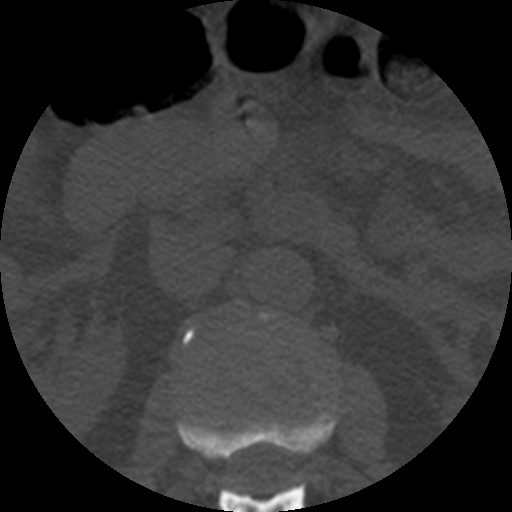
CT including the spine, one axial slice. Position 172 of 508 along the scan axis. Reconstruction kernel STANDARD. Bone window (W 1800 / L 400 HU). 1.25 mm slice thickness. 512 × 512 image matrix. Patient age 57 years. From the clinical record (not read from this slice): primary cancer: prostate.
Structures marked on this image (semi-automatic segmentation, software-assisted and operator-edited):
- L1 vertebra: bounding box <176,406,336,512> (left, top, right, bottom; pixels)
- L2 vertebra: <183,328,197,345>